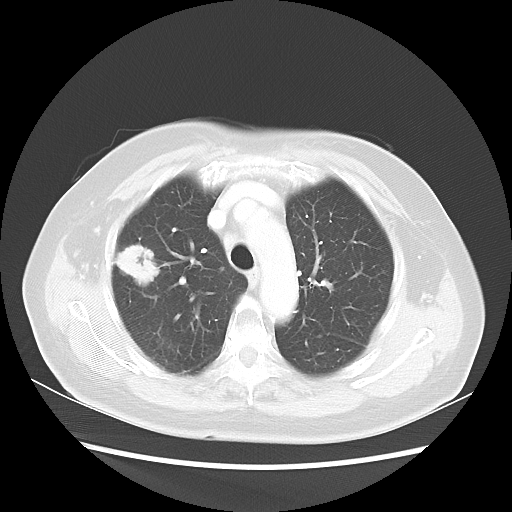
Chest CT, one axial slice. Position 35 of 48 along the scan axis. Reconstruction kernel LUNG. 100 kVp. Lung window (W 1500 / L -600 HU). 512 × 512 image matrix, field of view 360 × 360 mm. Patient: female, 75 years. Case-level facts recorded for this patient, not image findings: clinical TNM (as recorded): T1c N0 M0.
Structures marked on this image (rectangle marked by the reading radiologist):
- lung tumour (recorded histology: adenocarcinoma): bounding box [x1, y1, x2, y2] px = [111, 241, 158, 292]